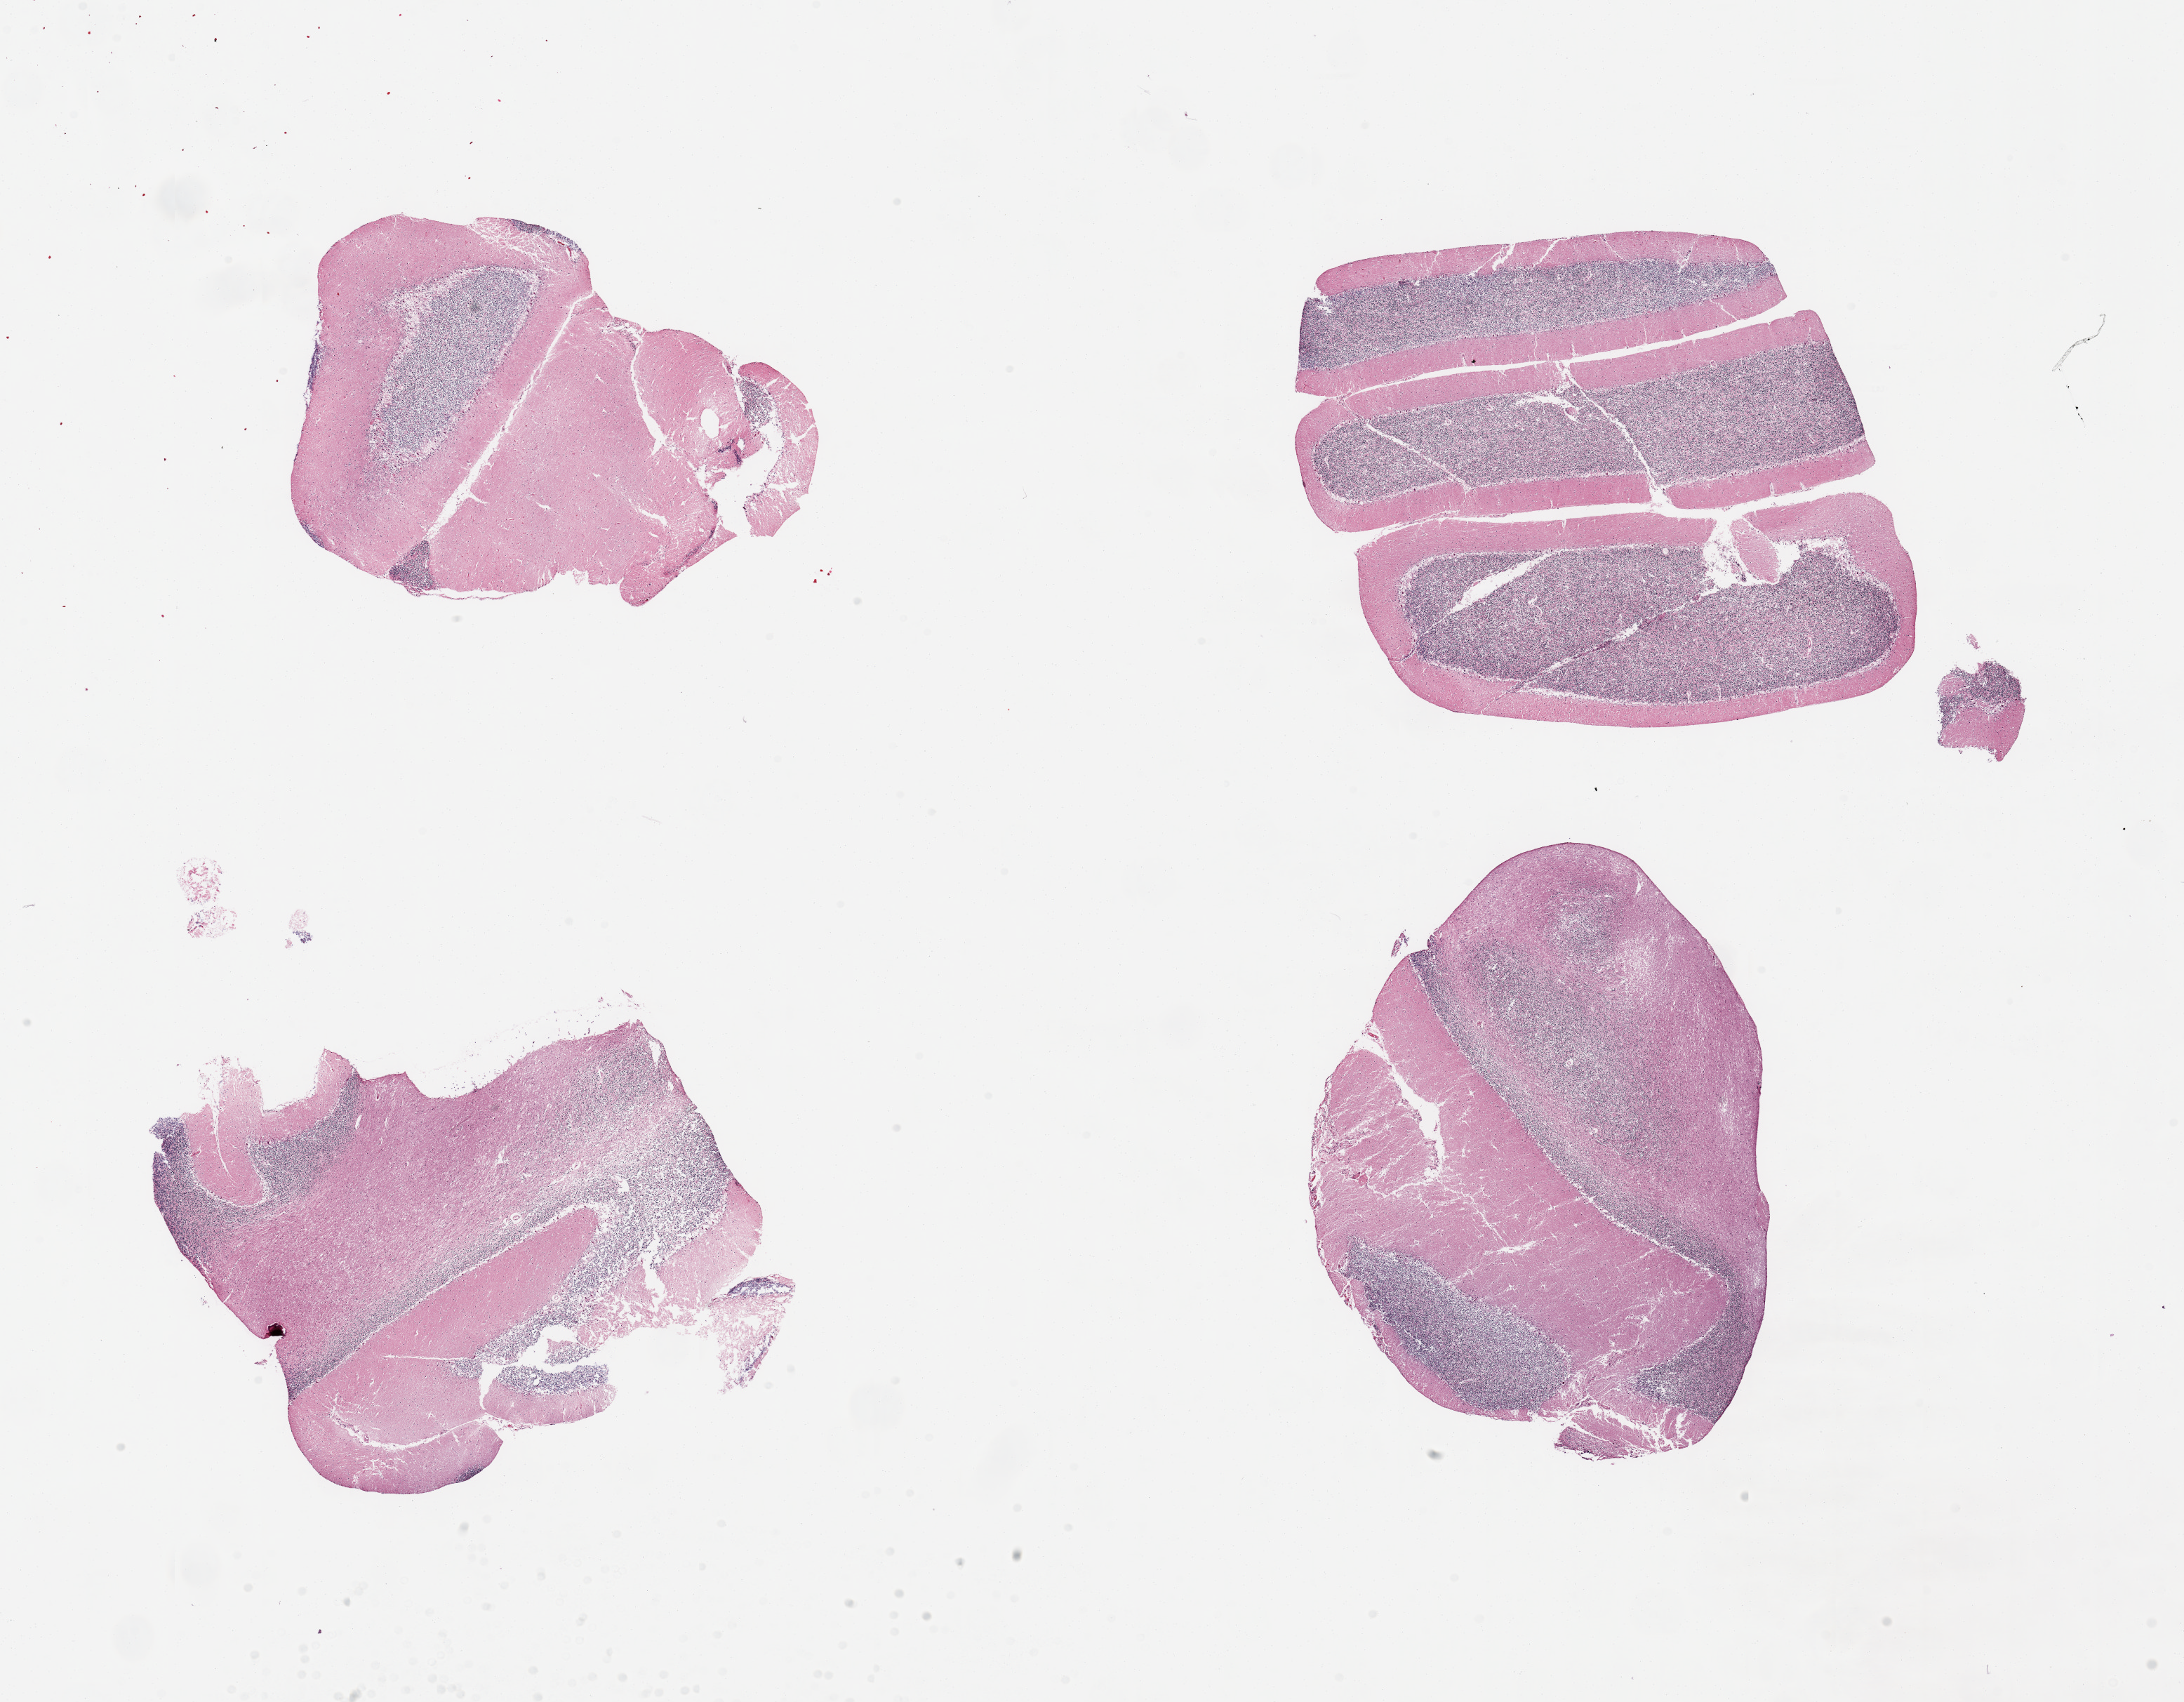
Digitized hematoxylin and eosin (H&E)-stained section, a low-resolution overview of the entire scanned area, about 24.6 x 19.2 mm; PAXgene-fixed, paraffin-embedded tissue; target tissue: cerebellum; tissue donor sample. Donor sex: female.
- pathologist's review note for this sample: 4 pieces, no abnormalities